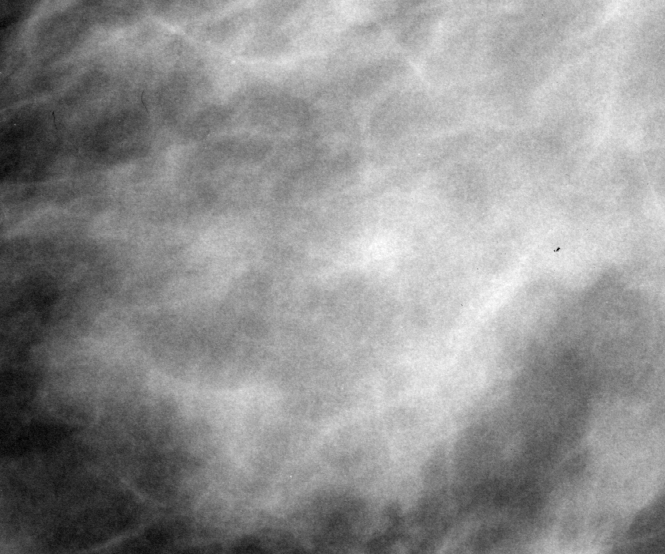
Crop from a digitized film mammogram around one marked abnormality, right breast, MLO view.
- Finding: mass, shape irregular / focal asymmetric density, margins ill defined; BI-RADS assessment category 3; subtlety rating 2 on a 1 (subtle) to 5 (obvious) scale; pathology result (as recorded, not read from the image): benign.